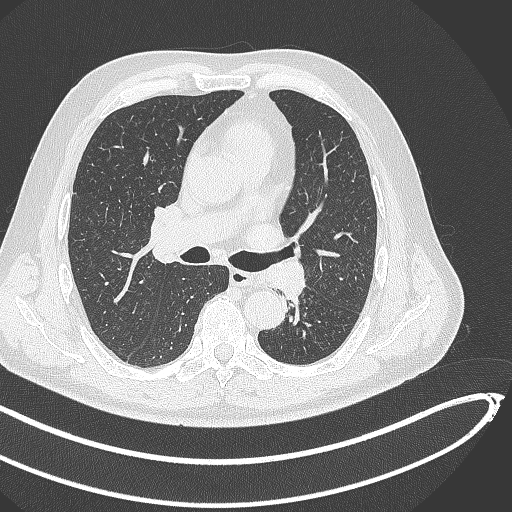
Chest CT, one axial slice. Reconstruction kernel B70f. Lung window (W 1500 / L -600 HU). 1 mm slice thickness. 512 × 512 image matrix. Male patient, age 64 years. From the clinical record (not read from this slice): clinical TNM (as recorded): T1c N0 M0.
Annotated regions visible in this slice (bounding box drawn by a radiologist):
- lung tumour (recorded histology: squamous cell carcinoma): box from (x=267, y=257) to (x=315, y=308) px